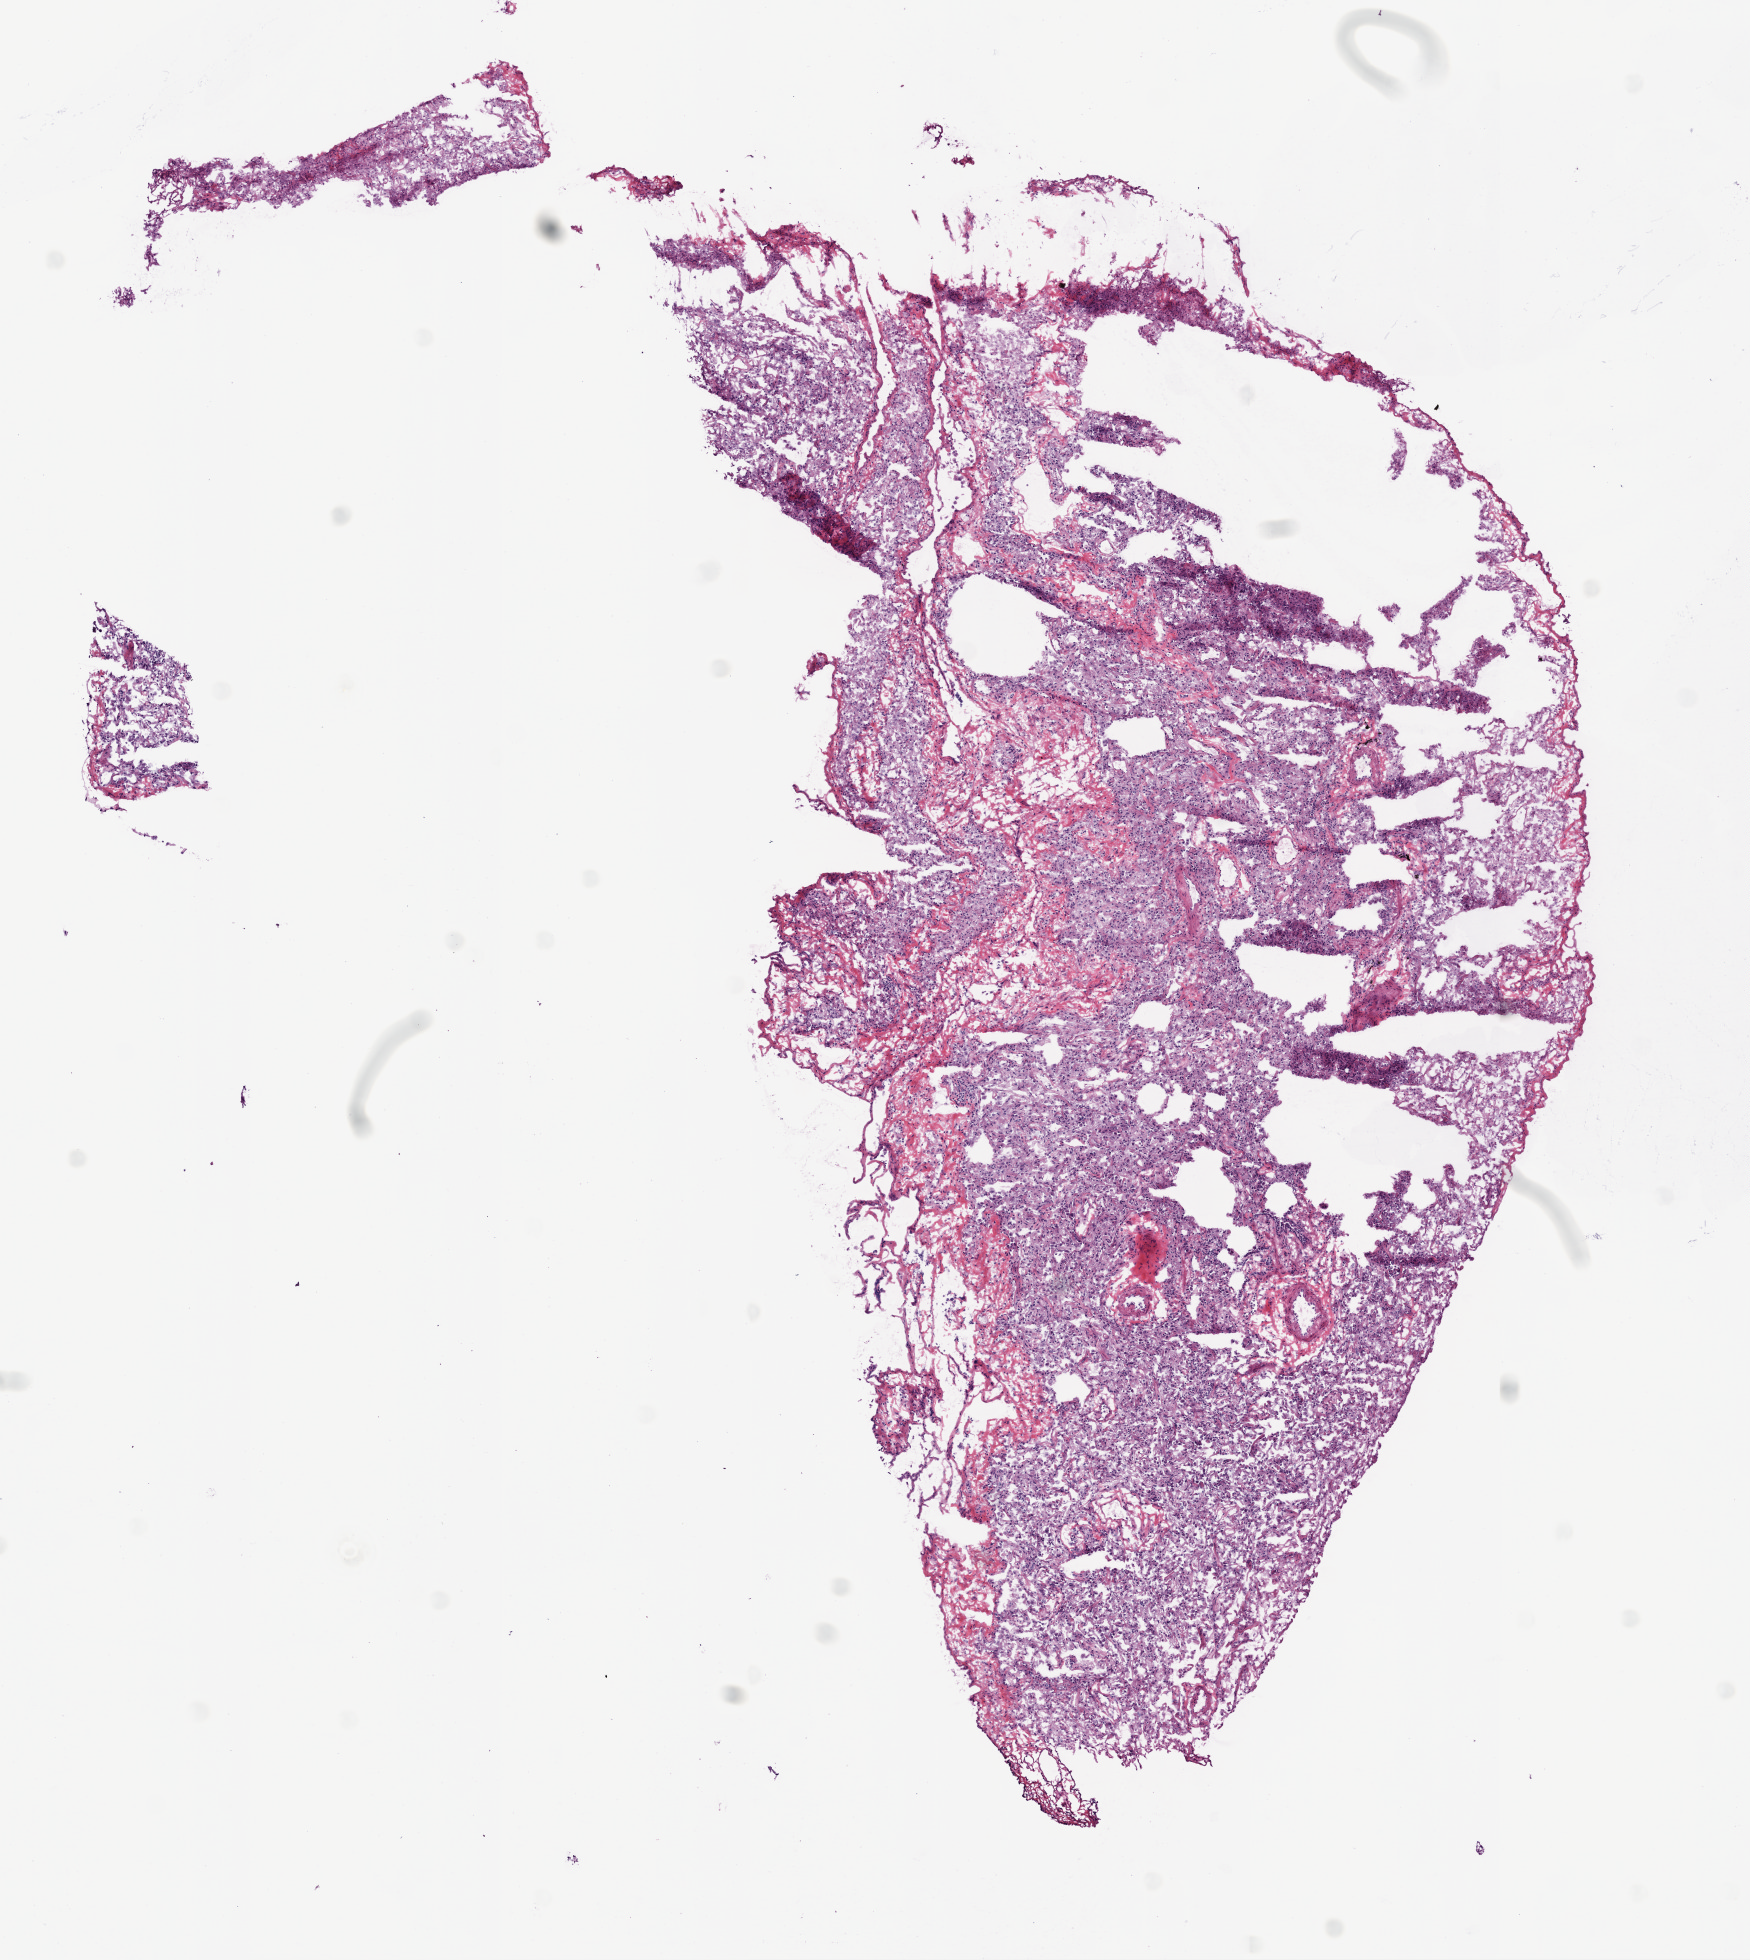
Digitized H&E tissue section (whole slide), a low-resolution overview of the entire scanned area, about 7.0 x 7.9 mm (slide scanned at 20x). Frozen section from the bottom of the tissue portion. Lung, solid tissue normal (non-tumour tissue) sample. Male, age 71 years at initial diagnosis.
This section: solid tissue normal (non-tumour) sample from the same patient. Patient diagnosis: Squamous cell carcinoma, NOS (upper lobe, lung).